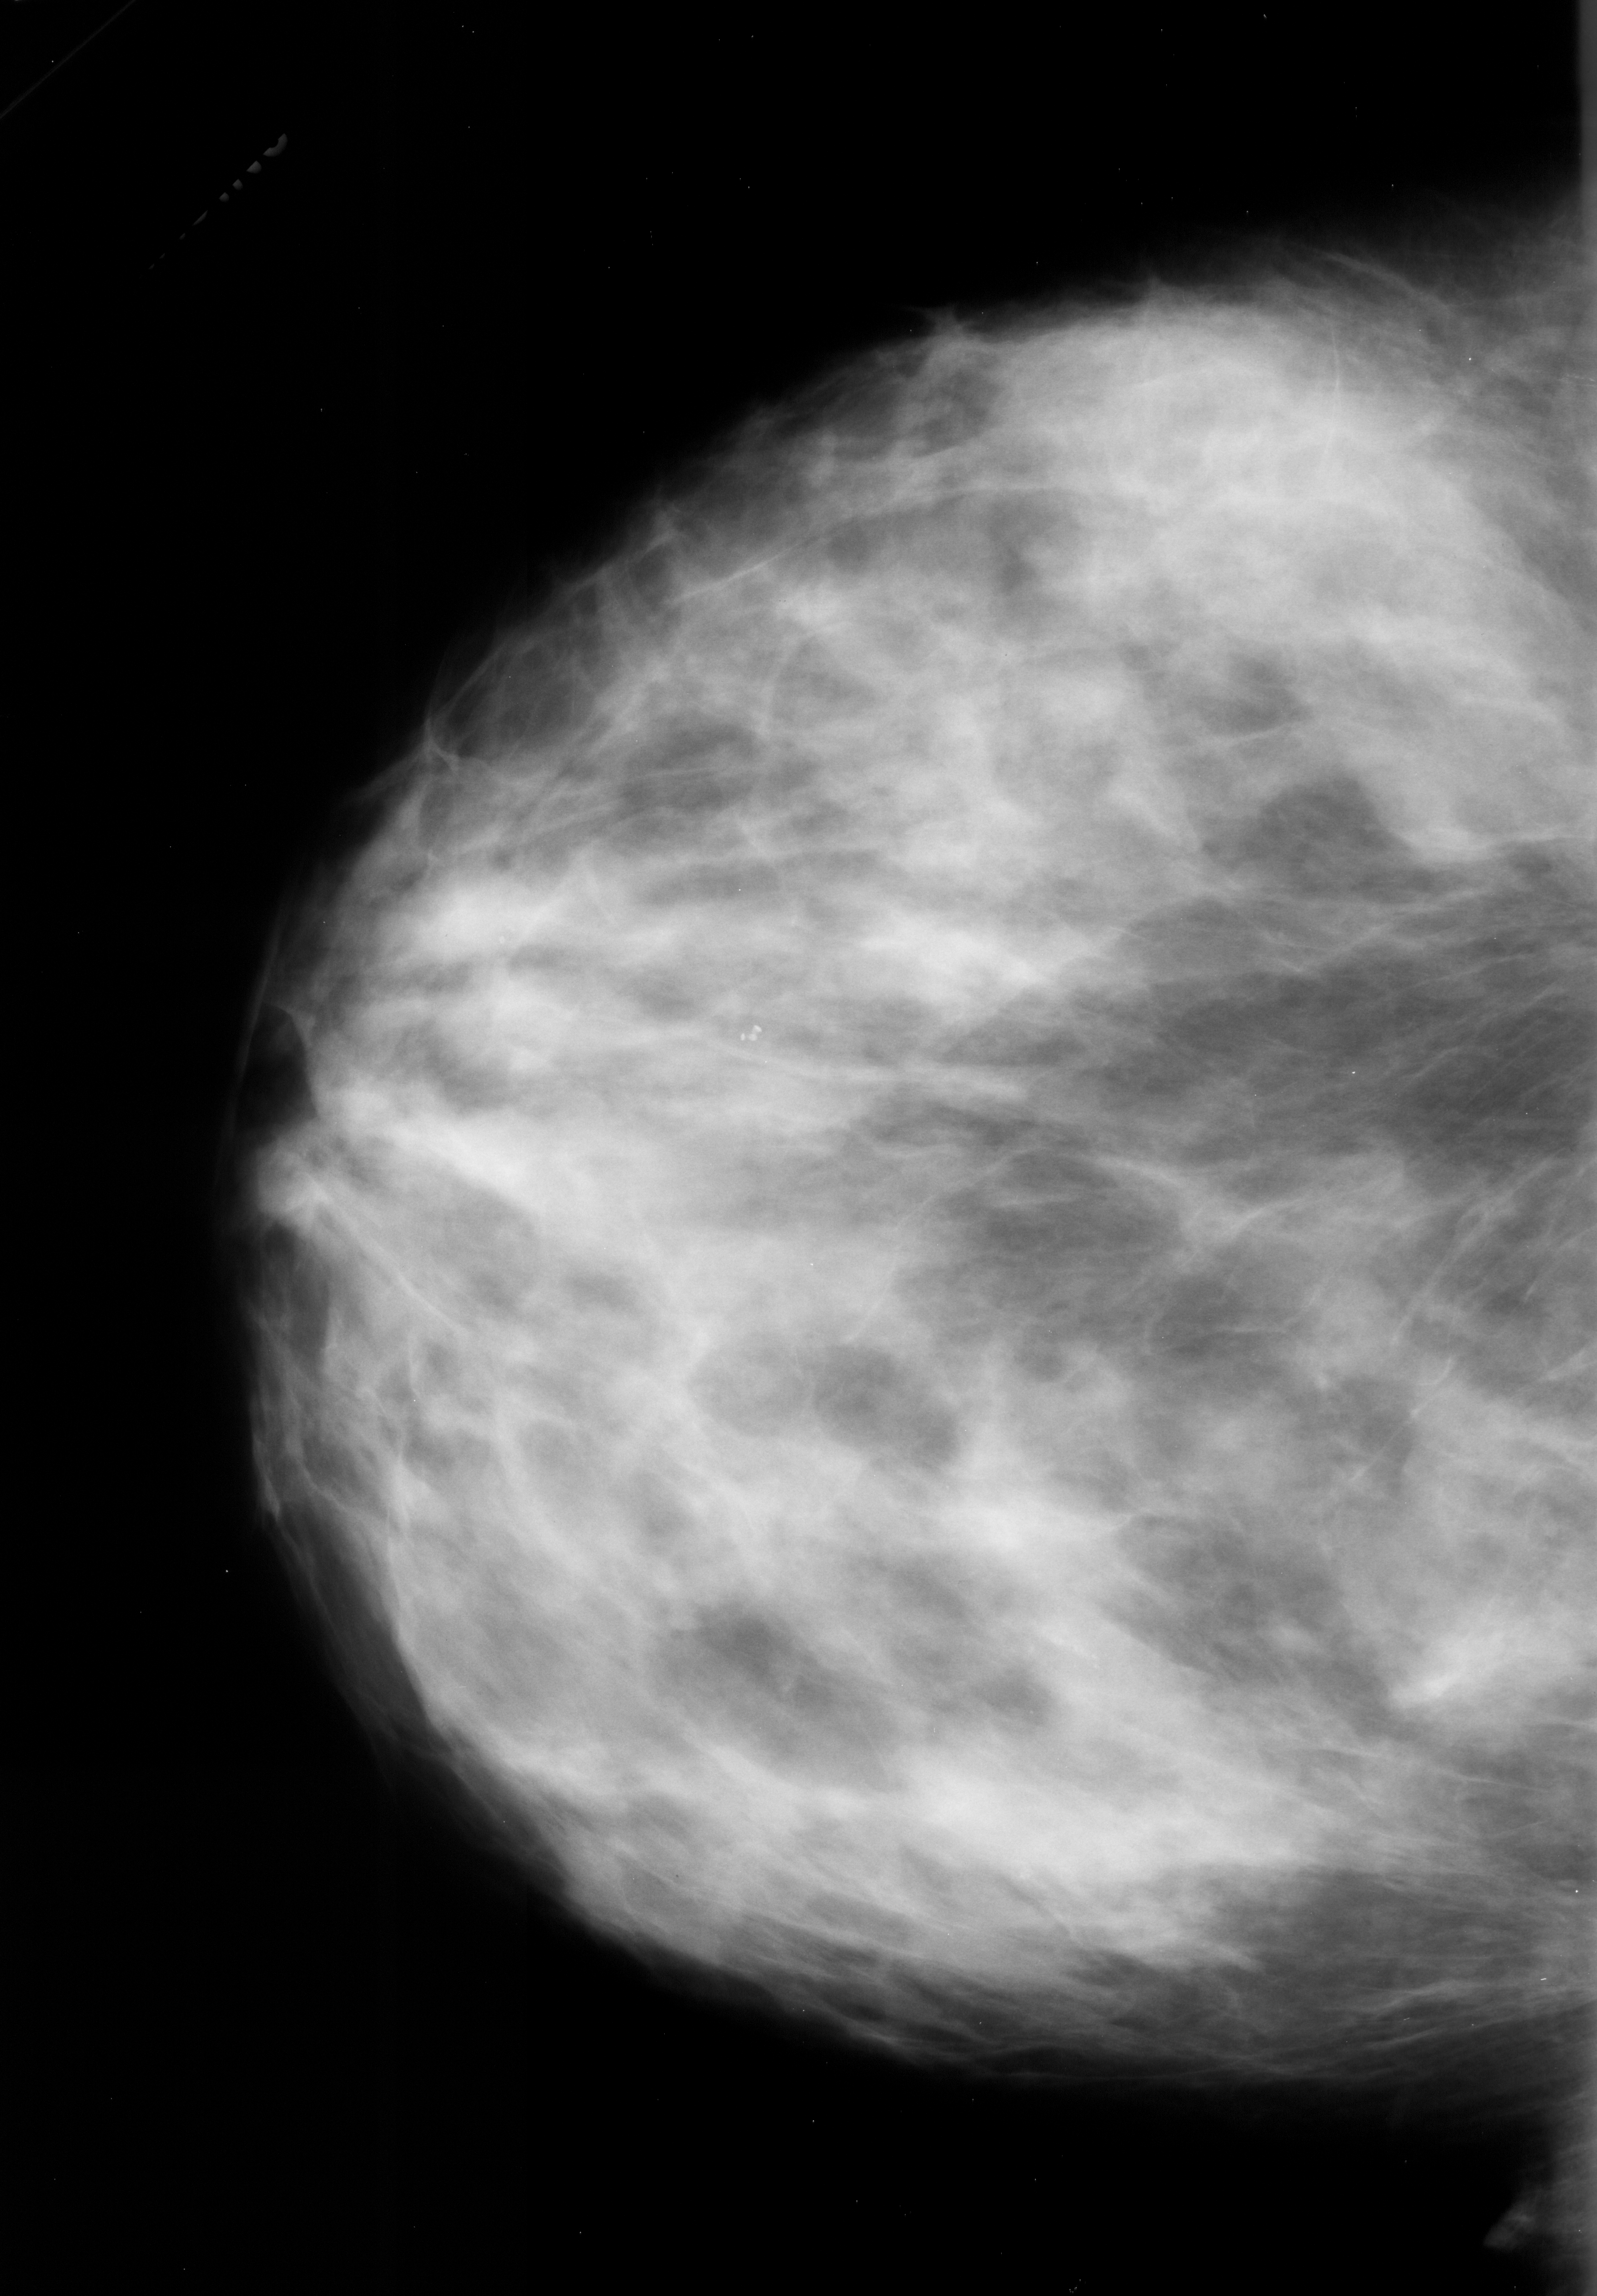
Digitized screen-film mammogram; left breast; CC view.
- Radiologist-marked abnormalities on this image: calcifications, morphology pleomorphic, distribution linear; BI-RADS assessment category 4; pathology result (as recorded, not read from the image): malignant.